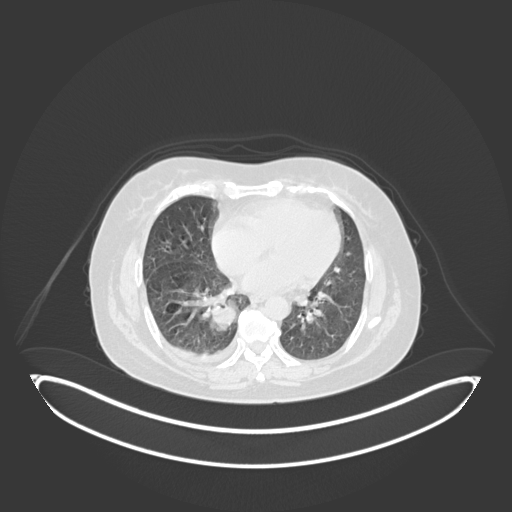
Chest CT, one axial slice; position 61 of 231 along the scan axis; reconstruction kernel B30f; lung window (W 1500 / L -600 HU); 512 × 512 image matrix, field of view 500 × 500 mm. Female patient, age 56 years. From the clinical record (not read from this slice): clinical TNM (as recorded): T2b N1 M0.
Outlined on this slice (bounding box drawn by a radiologist):
- lung tumour (recorded histology: small cell carcinoma): bounding box <212,300,245,340> (left, top, right, bottom; pixels)